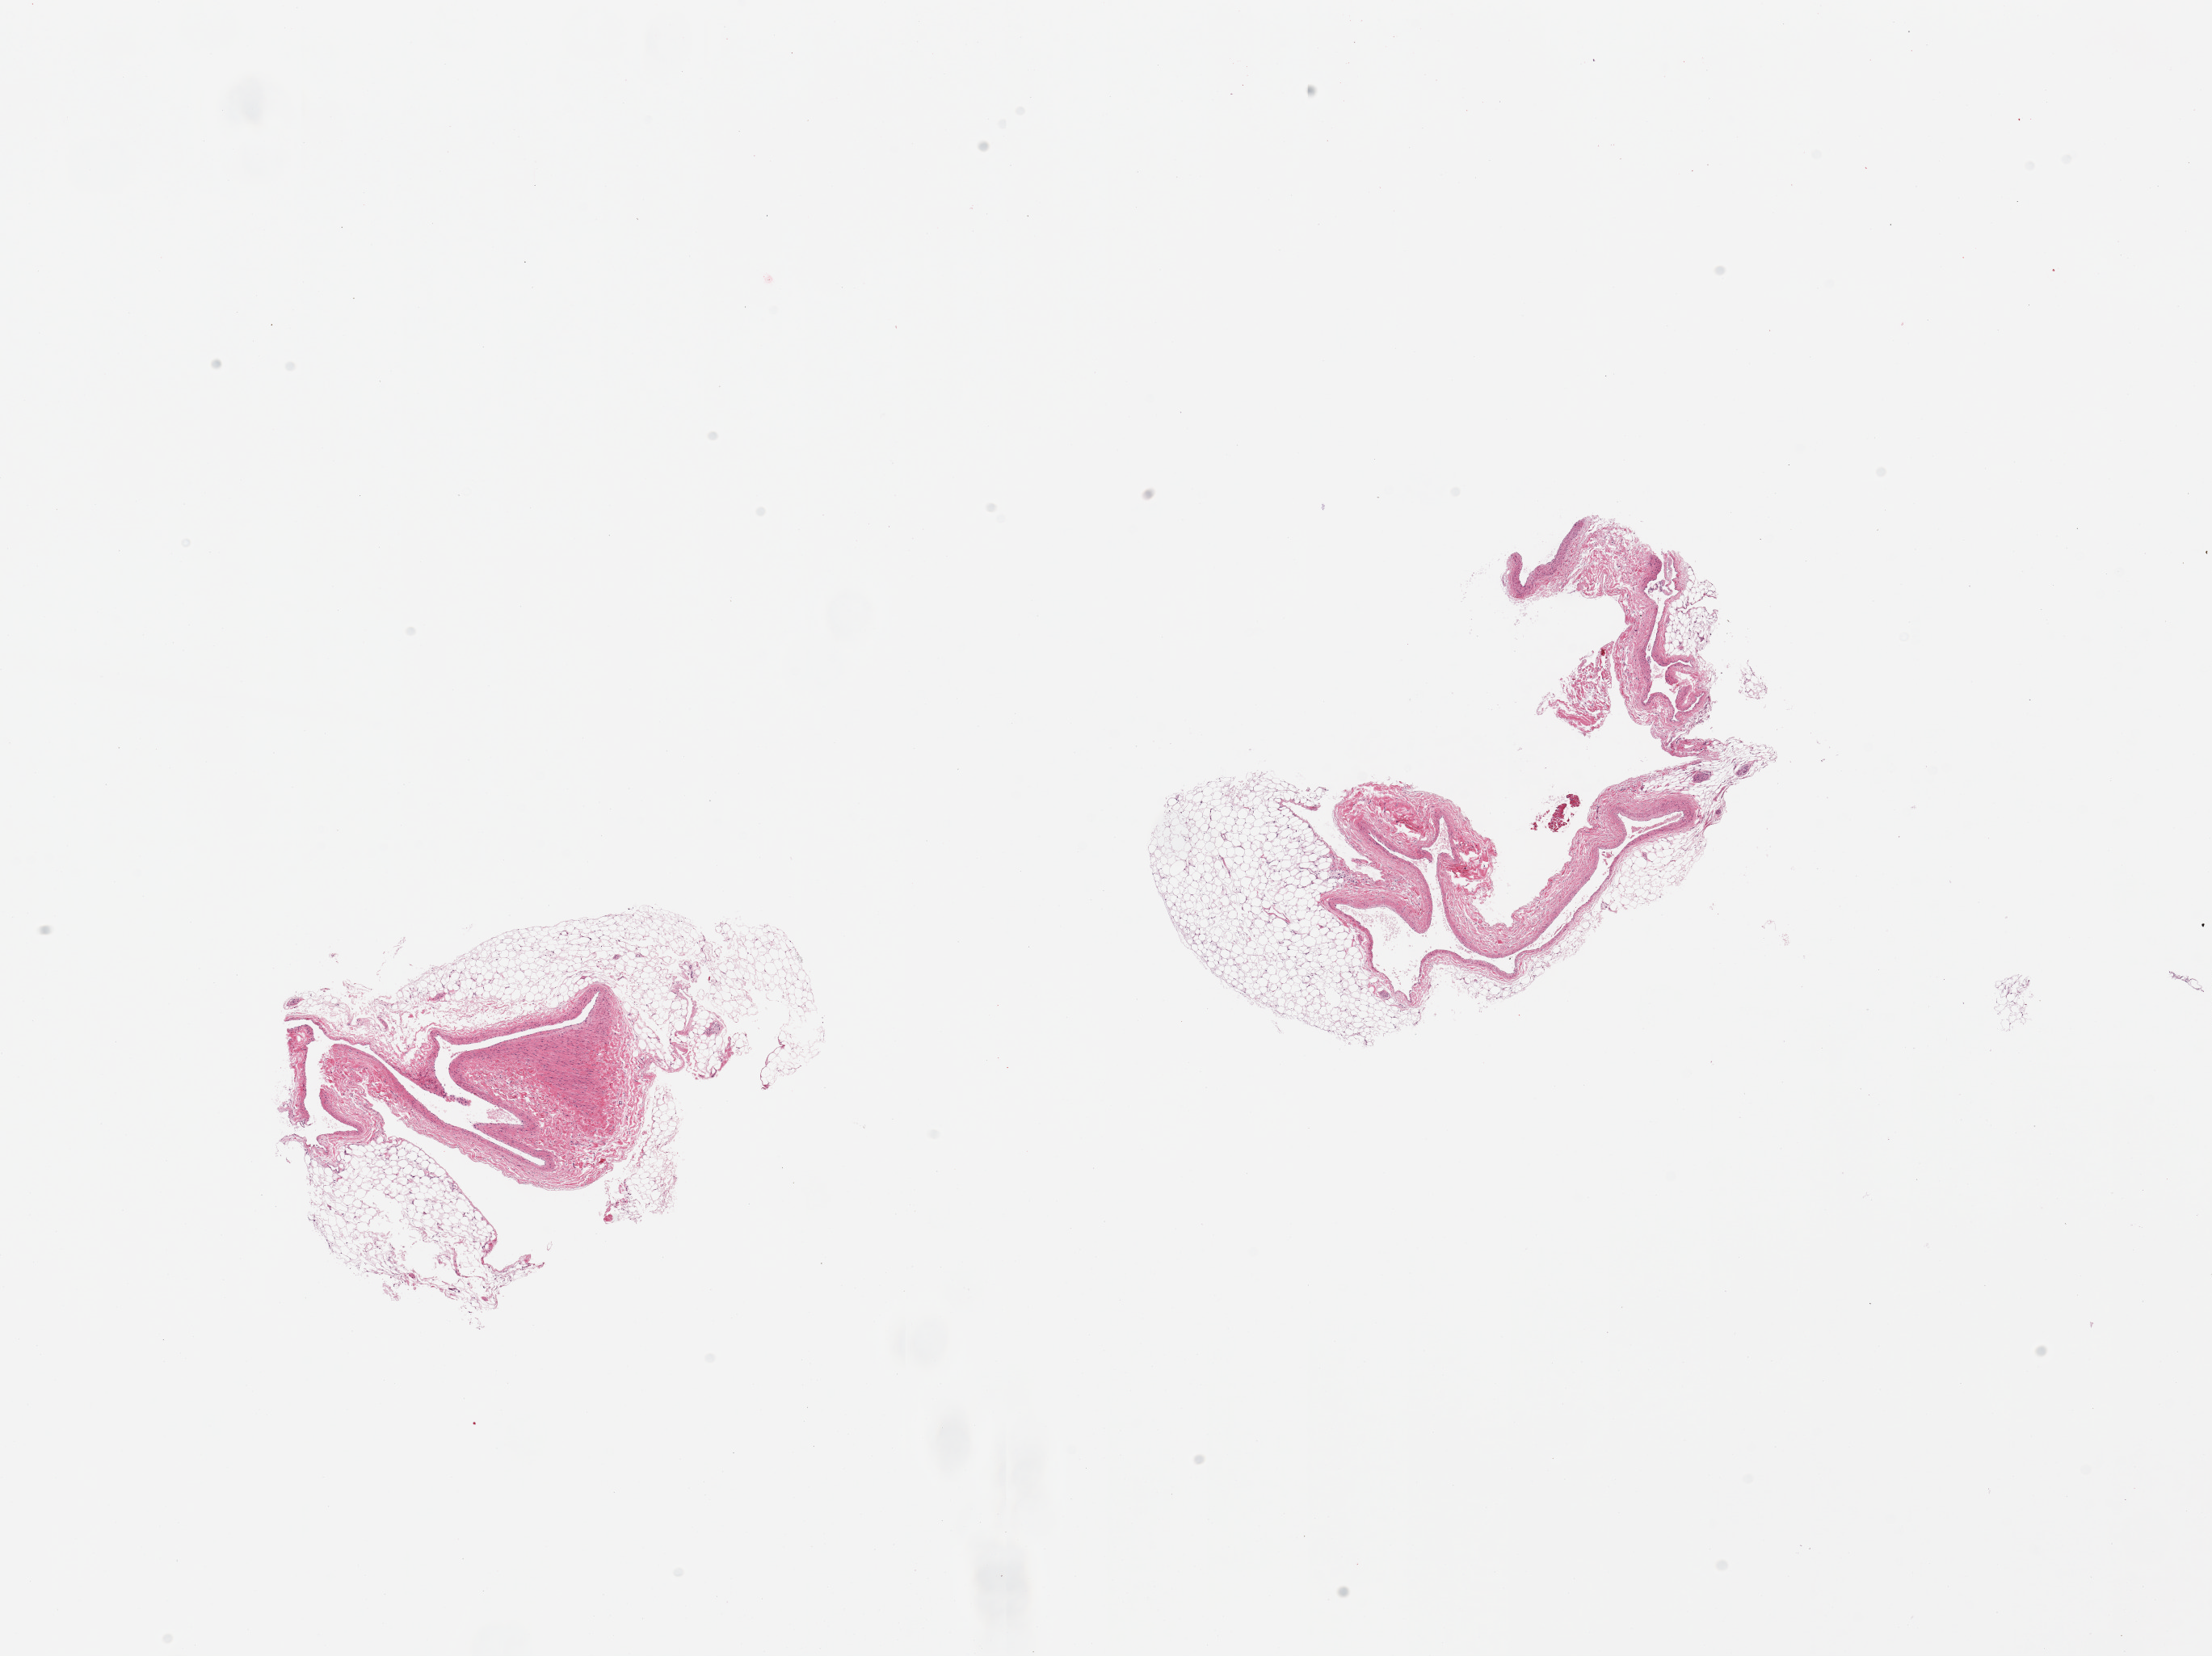
Digitized haematoxylin and eosin-stained section, low-resolution overview of the scanned area, about 21.7 x 16.2 mm. PAXgene-fixed, paraffin-embedded tissue. Sampled site (target tissue): coronary artery. Tissue donor sample. Donor: female.
* review note (as recorded): 2 pieces; veins and 50% perivascular fat